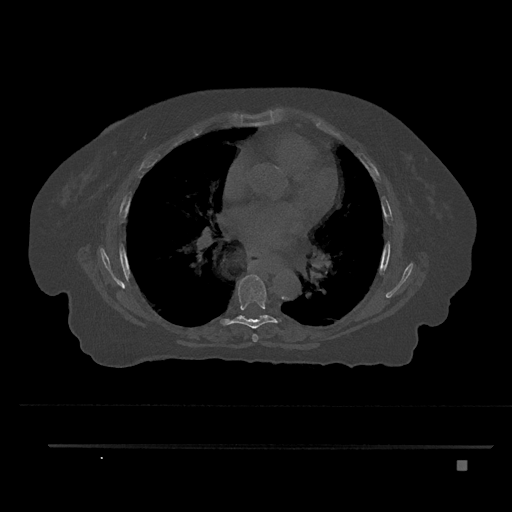
CT including the spine, one axial slice; position 488 of 797 along the scan axis; reconstruction kernel Br40s/3; bone window (W 1800 / L 400 HU); 0.5 mm slice thickness; 512 × 512 image matrix. Patient: female, 76 years. From the clinical record (not read from this slice): primary cancer: lung; vertebrae with lytic lesions (as recorded): T11, L3.
Outlined on this slice (semi-automatic segmentation, software-assisted and operator-edited):
- T6 vertebra: bounding box (x1, y1, x2, y2) in pixels: (252, 334, 259, 342)
- T7 vertebra: (221, 274, 282, 329)
- T8 vertebra: (240, 315, 268, 319)